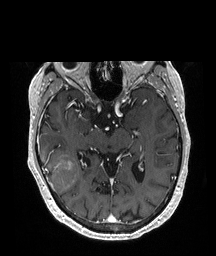
Brain MRI from a brain-tumour surgery series, one axial slice. Position 121 of 208 along the scan axis. T1-weighted post-contrast. 216 × 256 image matrix, field of view 216 × 256 mm. Case-level facts recorded for this patient, not image findings: histopathology: Glioblastoma; WHO grade: 4; IDH mutation: no.
Structures marked on this image (manually delineated by an expert):
- tumour: box from (x=39, y=150) to (x=78, y=195) px